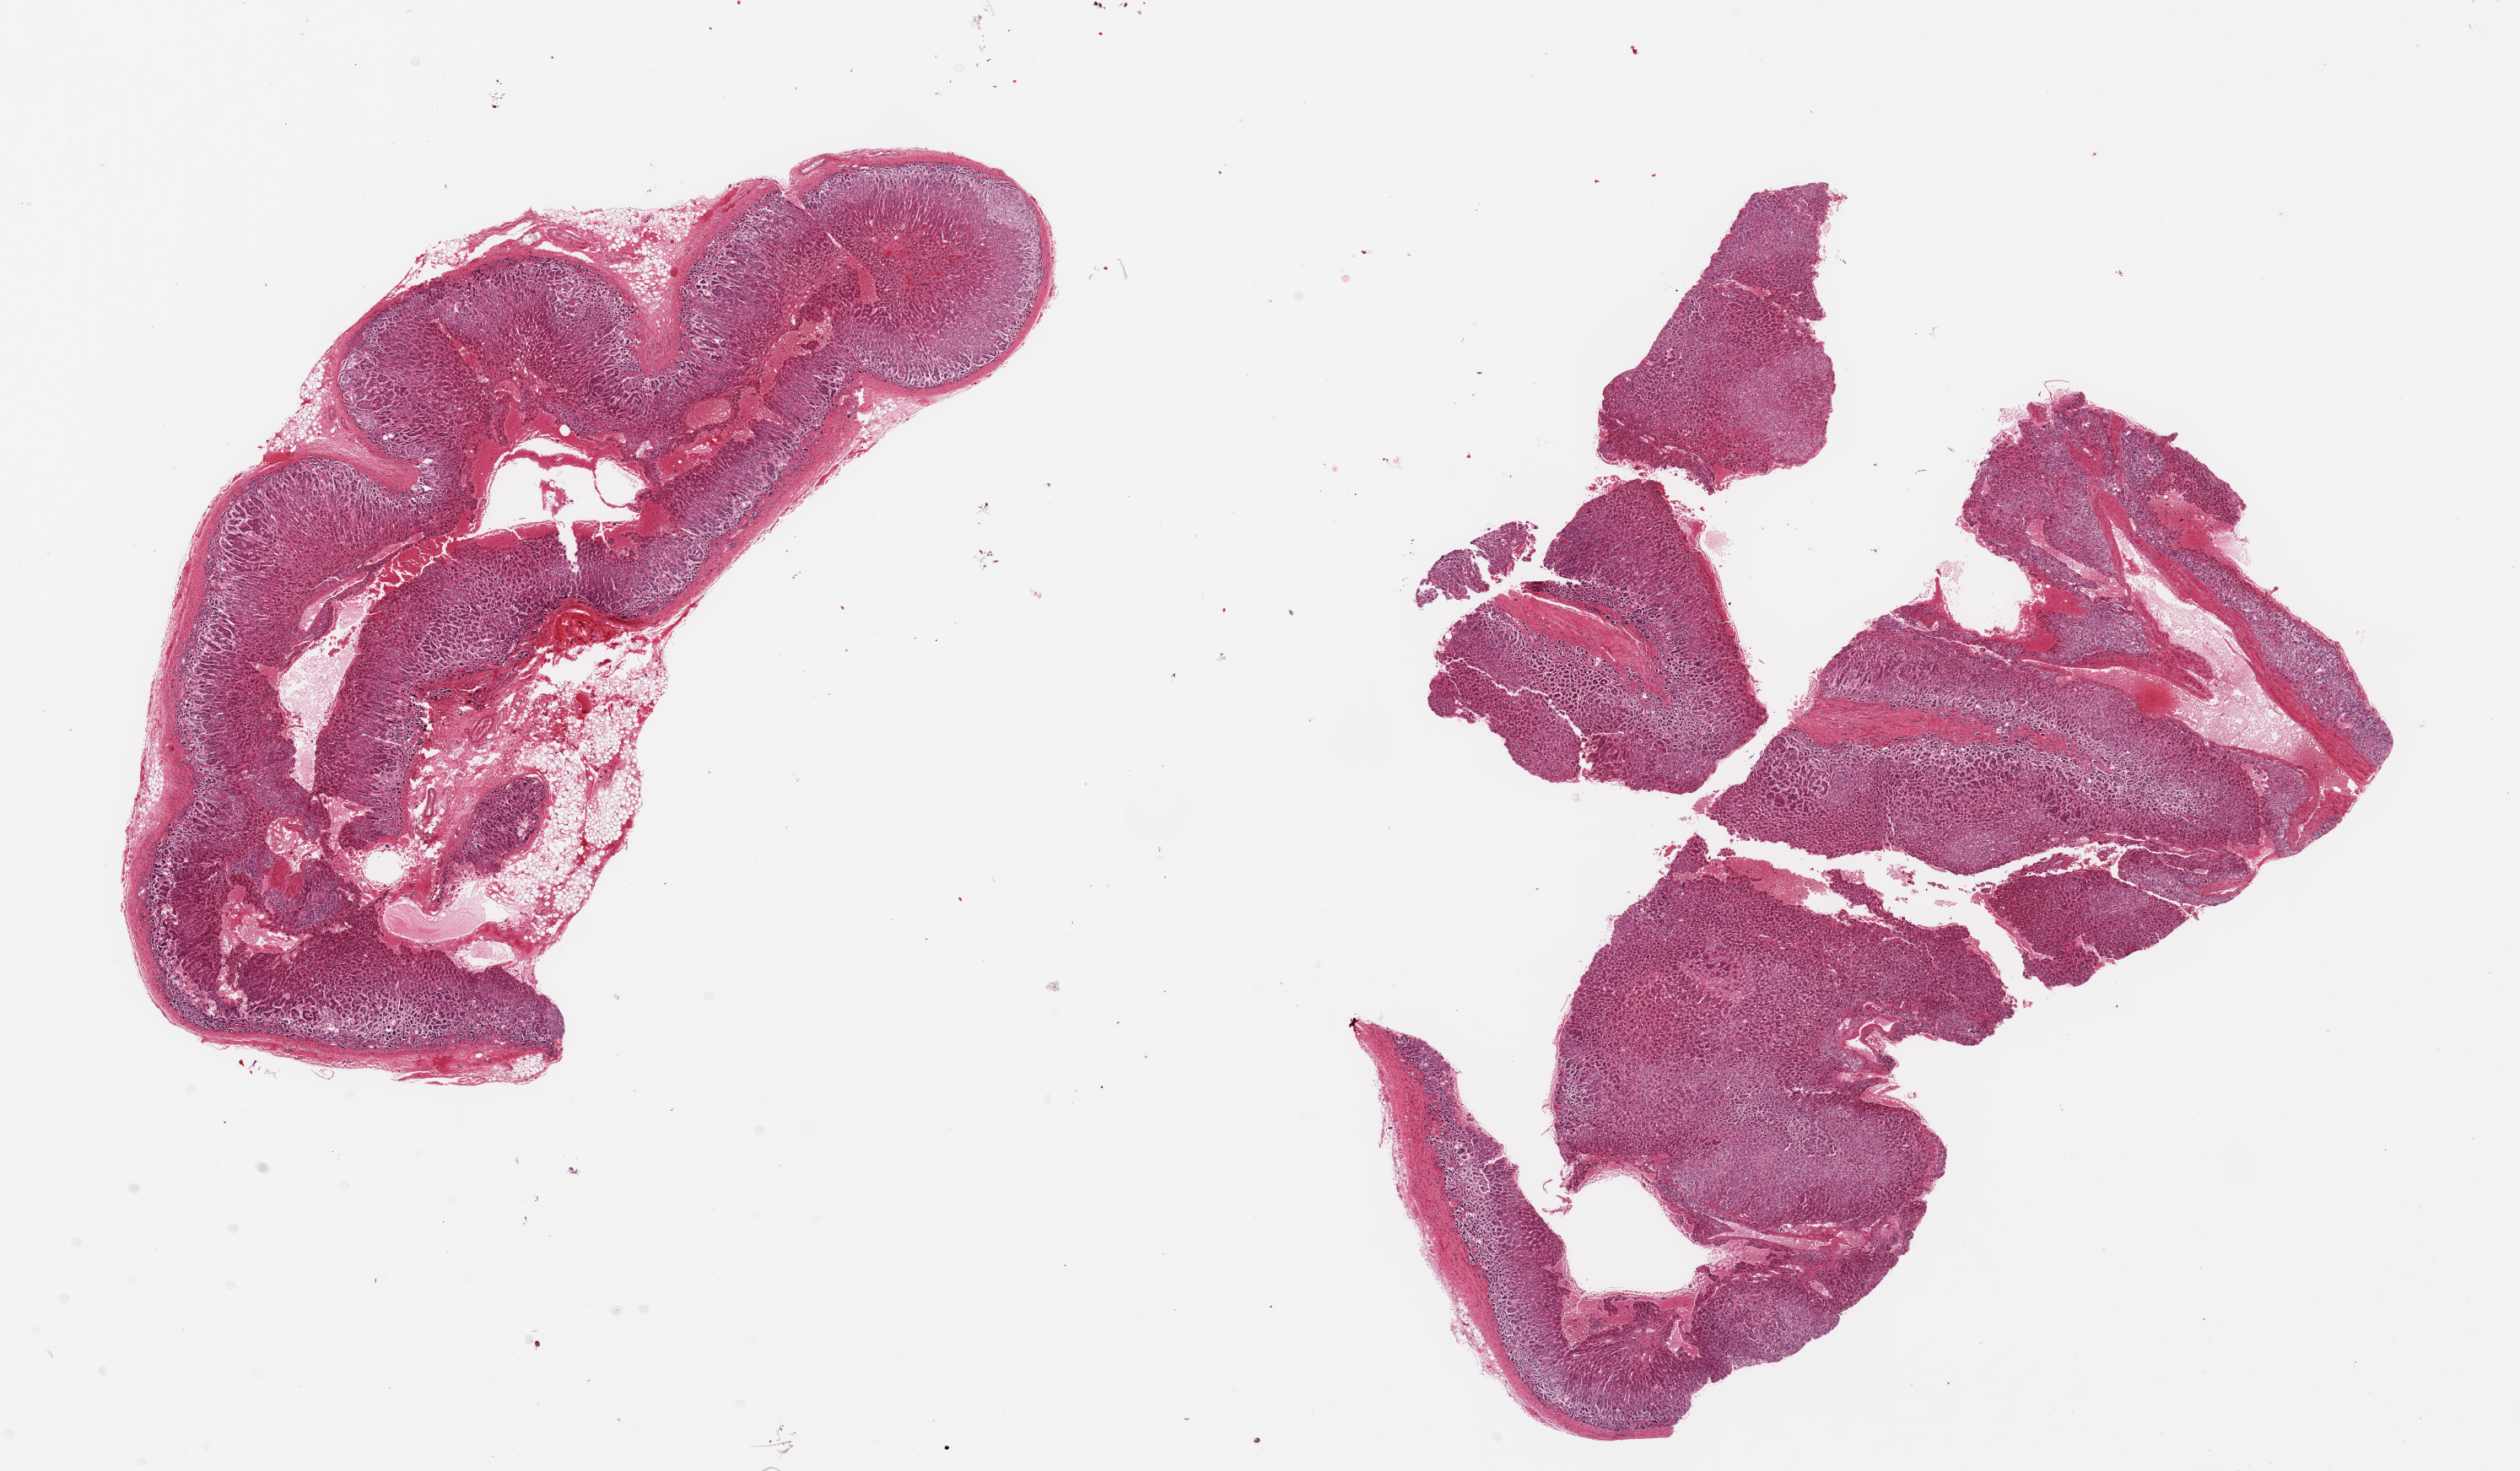
Haematoxylin and eosin whole-slide image, shown as a low-resolution overview of the whole scanned area (about 23.6 x 13.8 mm), PAXgene-fixed, paraffin-embedded tissue, section of adrenal gland (target tissue), tissue donor sample. Donor: female.
Reviewer comment on this tissue sample: 2 fragmented pieces; some foci are moderately autolyzed; 1 piece has 20% external fat.